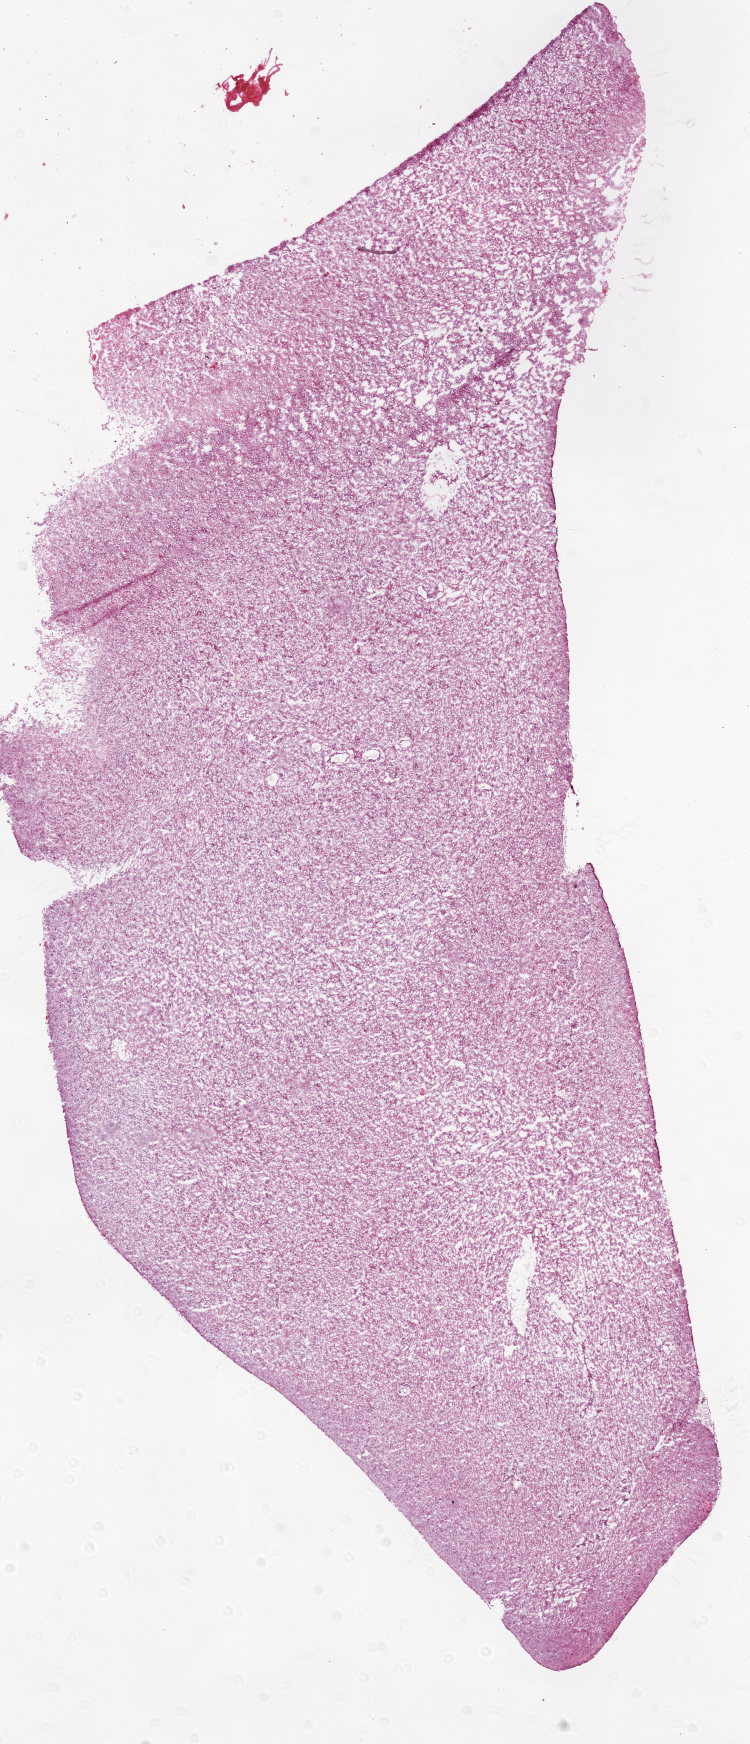
Whole-slide histology image, H&E-stained, shown as a low-resolution overview of the whole scanned area (about 6.0 x 14.0 mm, slide scanned at 20x); frozen section from the bottom of the tissue portion; primary tumour sample from the brain. Patient: male, age at initial diagnosis 61 years. Slide review estimates, as recorded: tumour cells 85%, tumour nuclei 90%, normal cells 5%, stromal cells 10%, necrosis 0%.
Histologic diagnosis: Glioblastoma.